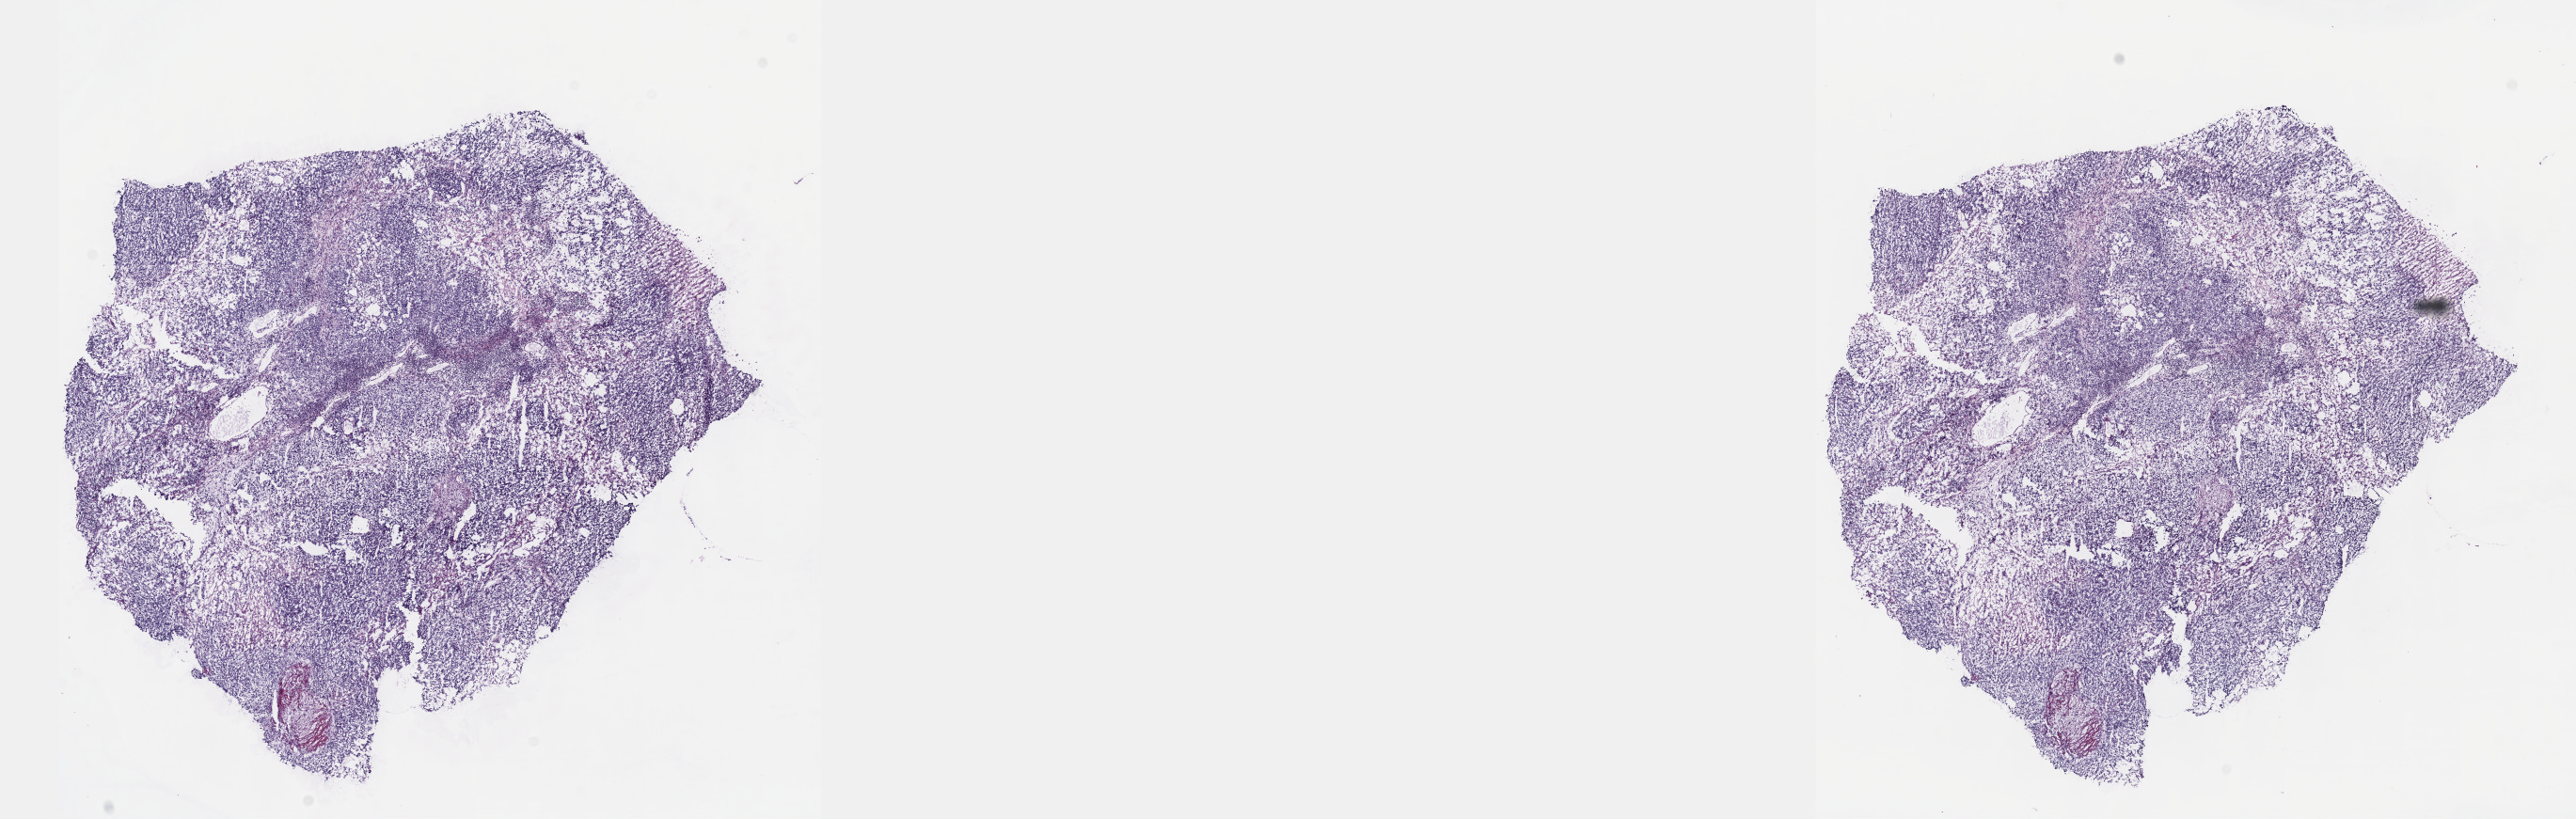
H&E whole-slide image, whole scanned area (about 22.1 x 7.0 mm) shown as a low-resolution overview. Male patient. Pathologist review of this section (percent, as recorded): tumour cells 100%, tumour nuclei 80%, normal cells 0%, stromal cells 0%, necrosis 0%. Inflammatory infiltration, as recorded: lymphocyte infiltration 1%, monocyte infiltration 0%, neutrophil infiltration 0%.
- specimen: frozen section from the top of the tissue portion; sample: primary tumour, testis